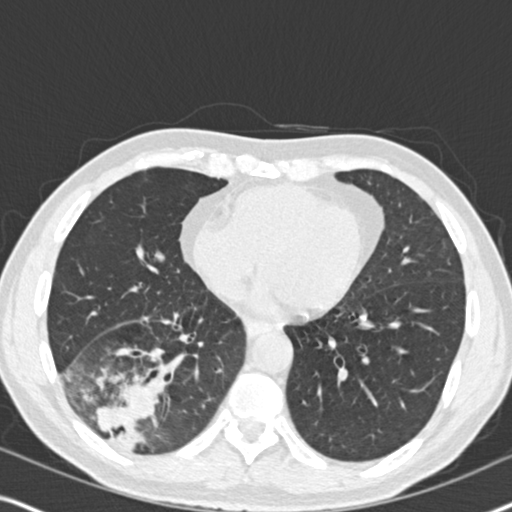
Low-dose screening chest CT, one axial slice; position 77 of 182 along the scan axis; reconstruction kernel B30f; 120 kVp; lung window (W 1500 / L -600 HU); 2 mm slice thickness; 512 × 512 image matrix, field of view 330 × 330 mm.
Annotated regions visible in this slice (outlined manually by an expert reader):
- lesion 1 (tumor, lower lobe of right lung): bounding box <96,382,161,446> (left, top, right, bottom; pixels)